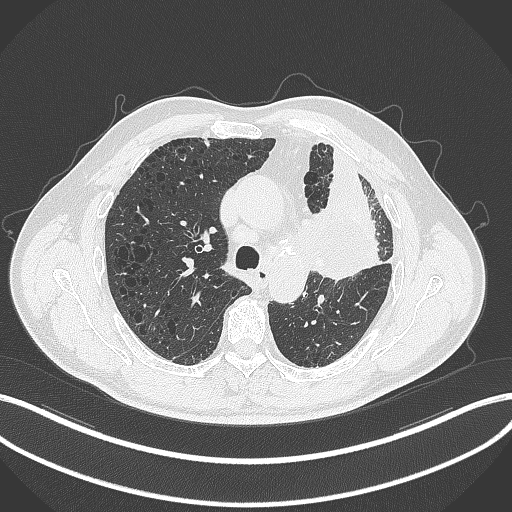
Chest CT, one axial slice. Slice 212 of 297 in the series (ordered by position). Reconstruction kernel B70f. 120 kVp. Lung window (W 1500 / L -600 HU). 1 mm slice thickness. 512 × 512 image matrix, field of view 400 × 400 mm. Patient: male, 68 years. From the clinical record (not read from this slice): clinical TNM (as recorded): T3 N3 M1.
Structures marked on this image (bounding box drawn by a radiologist):
- lung tumour (recorded histology: adenocarcinoma): bounding box (x1, y1, x2, y2) in pixels: (313, 194, 392, 289)